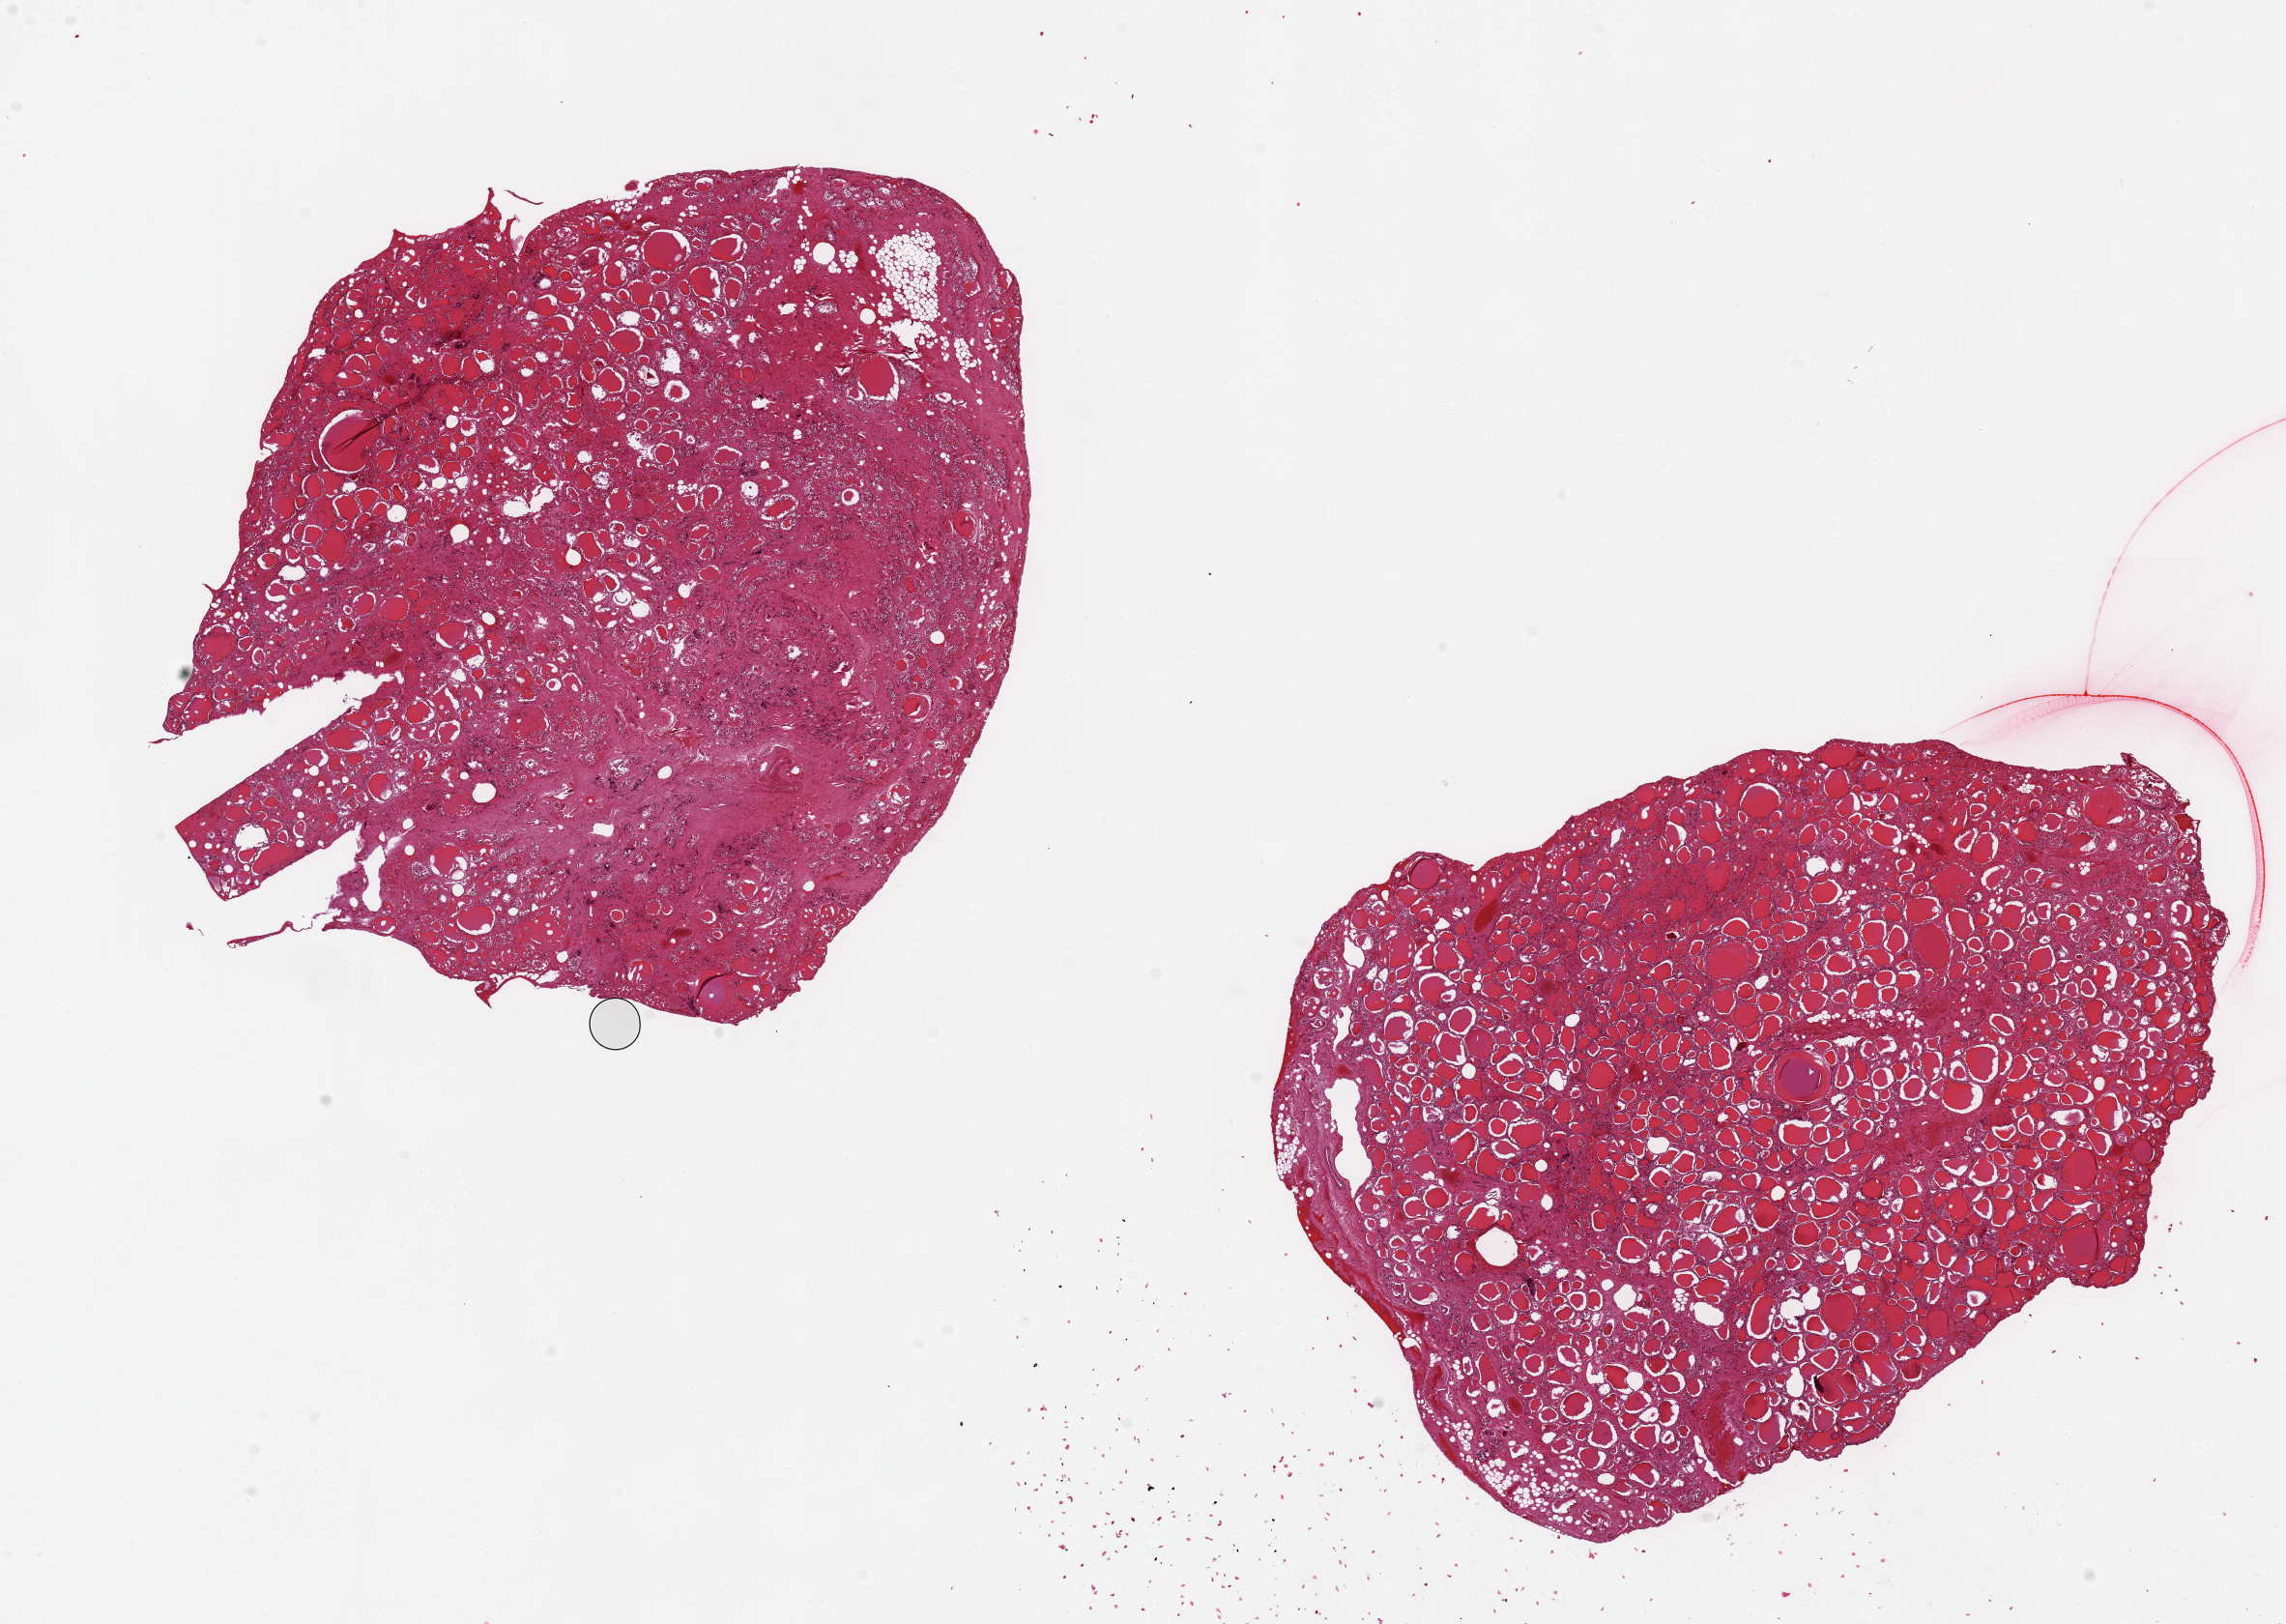
Whole-slide image, H&E stain — whole scanned area (about 18.7 x 13.3 mm) shown as a low-resolution overview, PAXgene-fixed, paraffin-embedded tissue, section of thyroid (target tissue), tissue donor sample. Donor sex: male.
Review note (as recorded): 2pieces ~8x6mm, unusually badly autolyzed.